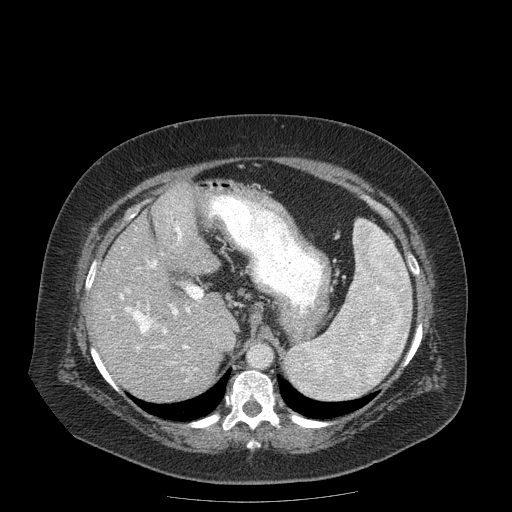
Contrast-enhanced abdominal CT (liver protocol), one axial slice; slice 119 of 204 in the series (ordered by position); soft-tissue window (W 400 / L 40 HU); 2.5 mm slice thickness; 512 × 512 image matrix, field of view 440 × 440 mm. From the clinical record (not read from this slice): diagnosis: hepatocellular carcinoma (patient treated with transarterial chemoembolisation; whether this scan precedes or follows treatment is not stated here); TNM stage (as recorded): Stage-IIIB; Child-Pugh class: A; tumour differentiation: well differentiated; tumour nodularity: uninodular.
Structures marked on this image (semi-automatic segmentation, software-assisted and operator-edited):
- abdominal aorta: bounding box (x1, y1, x2, y2) in pixels: (249, 345, 271, 367)
- liver parenchyma outside the tumour (the mass and vessels are separate outlines, so this box may not span the whole liver): (92, 182, 236, 400)
- liver vessels: (111, 206, 203, 381)